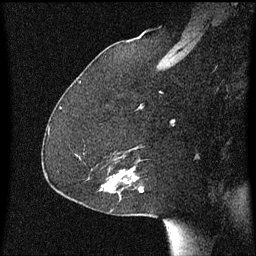
Breast MRI (dynamic contrast-enhanced), one sagittal slice. Slice 40 of 60 in the series (ordered by position). Dynamic contrast-enhanced series, image 2 of 3 at this slice position (ordered by acquisition). 1.5 T. TE 4.2 ms, TR 8.4 ms. 256 × 256 image matrix. Female patient, age 59 years.
Annotated regions visible in this slice (semi-automatically segmented with operator editing):
- analysis volume of interest (the breast-tissue region the enhancement analysis was run in; not a lesion): bounding box <100,168,143,199> (left, top, right, bottom; pixels)
- tumour enhancement mask (voxels above the 70 % enhancement threshold inside the analysis volume of interest): <110,170,143,193>